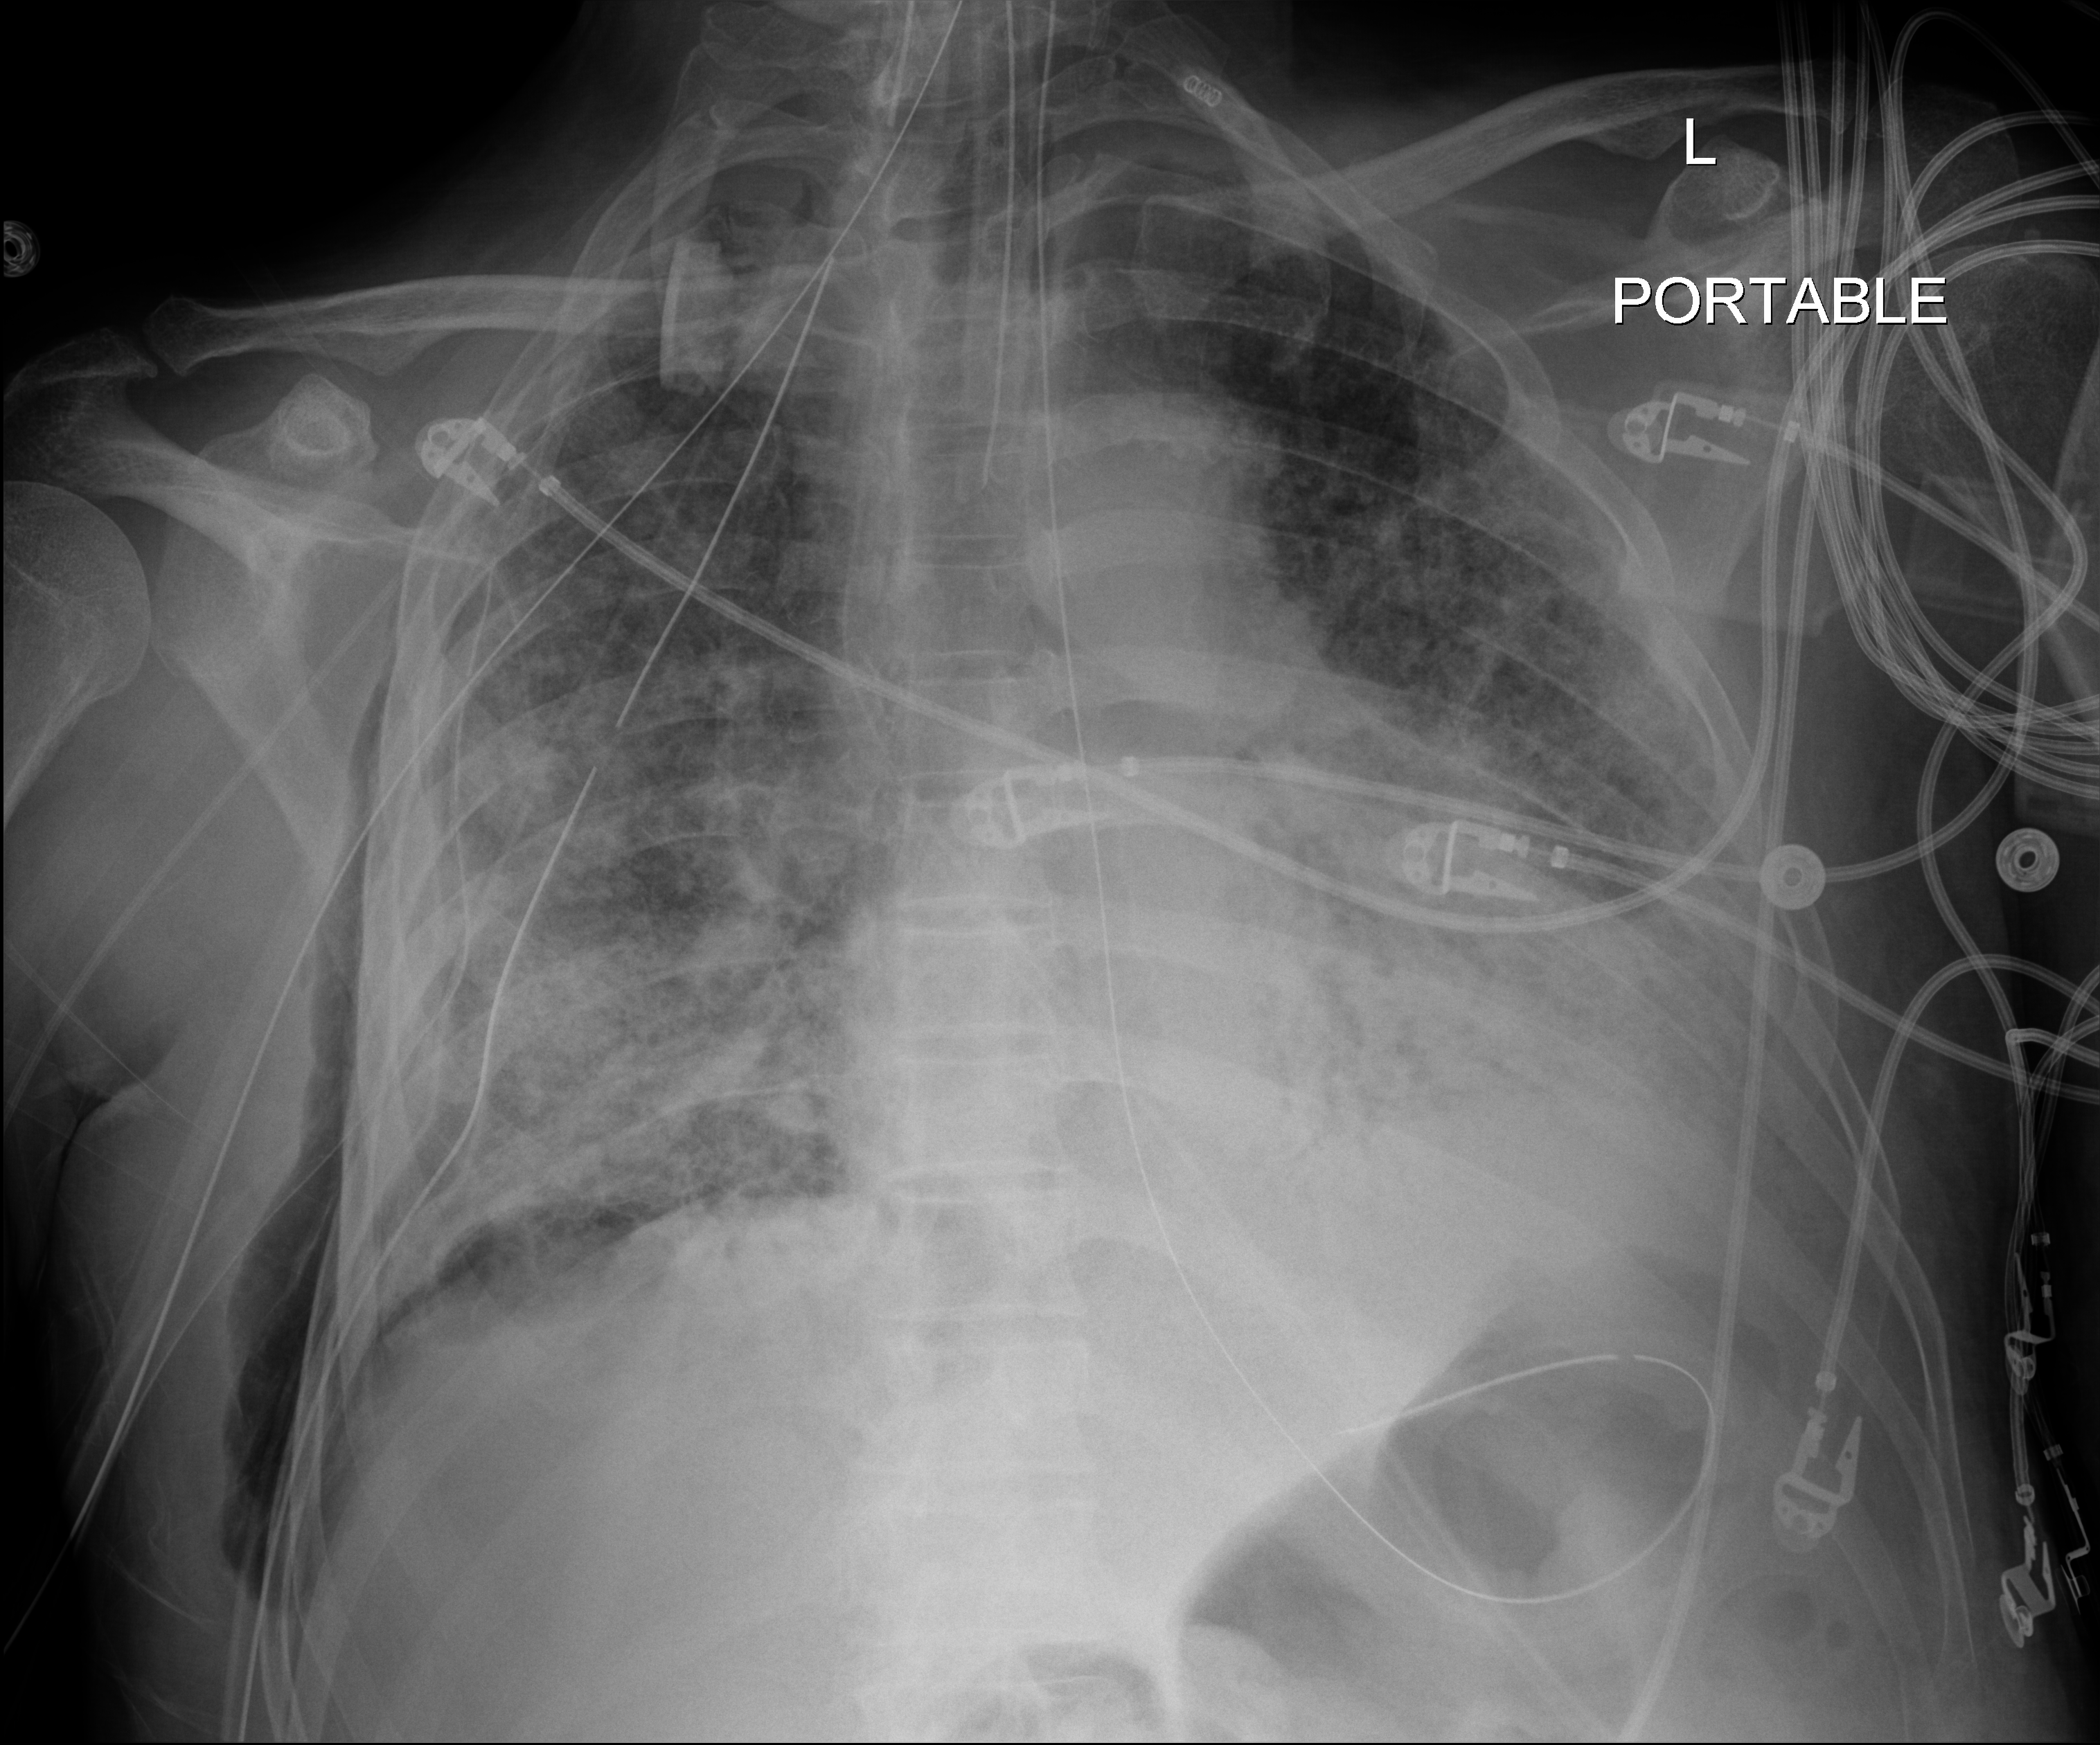
Chest X-ray (portable); anteroposterior (AP) projection. Patient hospitalised with COVID-19; male, aged 60–74 years.
From the hospital-stay record, not from the radiograph (when in the stay this image was taken is not recorded): chronic kidney disease (admission record): no; length of hospital stay: 37 days; admitted to intensive care during this hospital stay: yes.